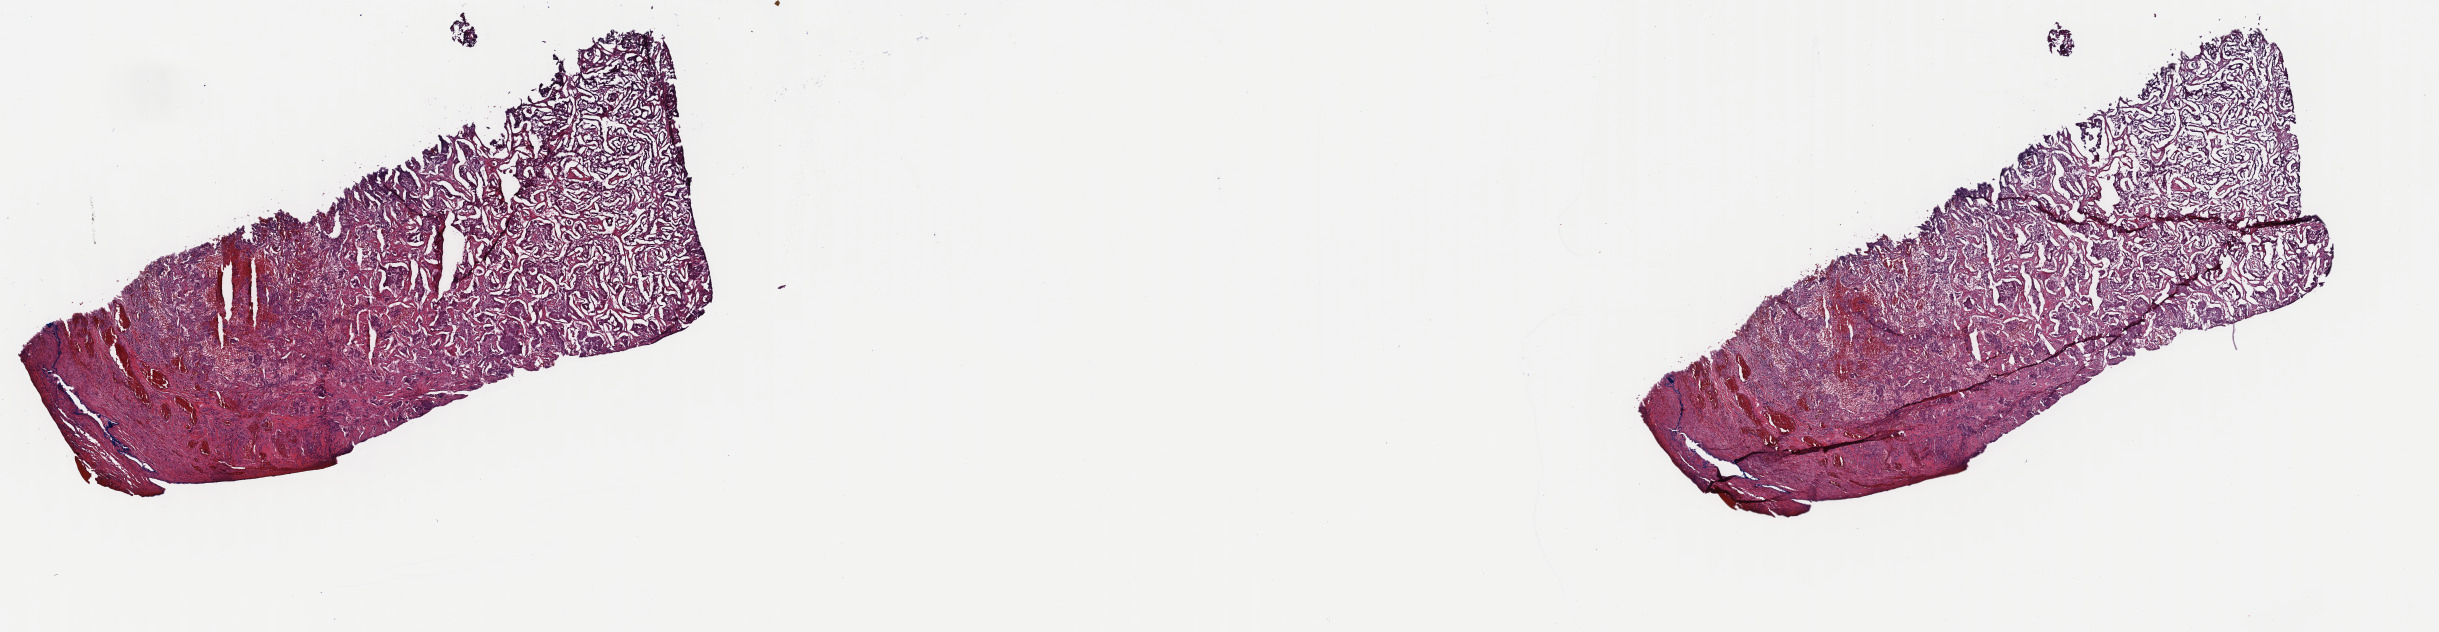
Whole-slide histology image, H&E, a low-resolution overview of the entire scanned area, about 19.2 x 5.0 mm, frozen section from the top of the tissue portion, sample: primary tumour, lung. Female patient; age at initial diagnosis 50 years. Pathologist review of this section (percent, as recorded): tumour cells 80%, tumour nuclei 80%, normal cells 0%, stromal cells 20%, necrosis 0%. Inflammatory infiltration, as recorded: lymphocyte infiltration 0%, monocyte infiltration 0%, neutrophil infiltration 0%.
Diagnosis: Adenocarcinoma with mixed subtypes (upper lobe, lung). AJCC pathologic stage: IA.